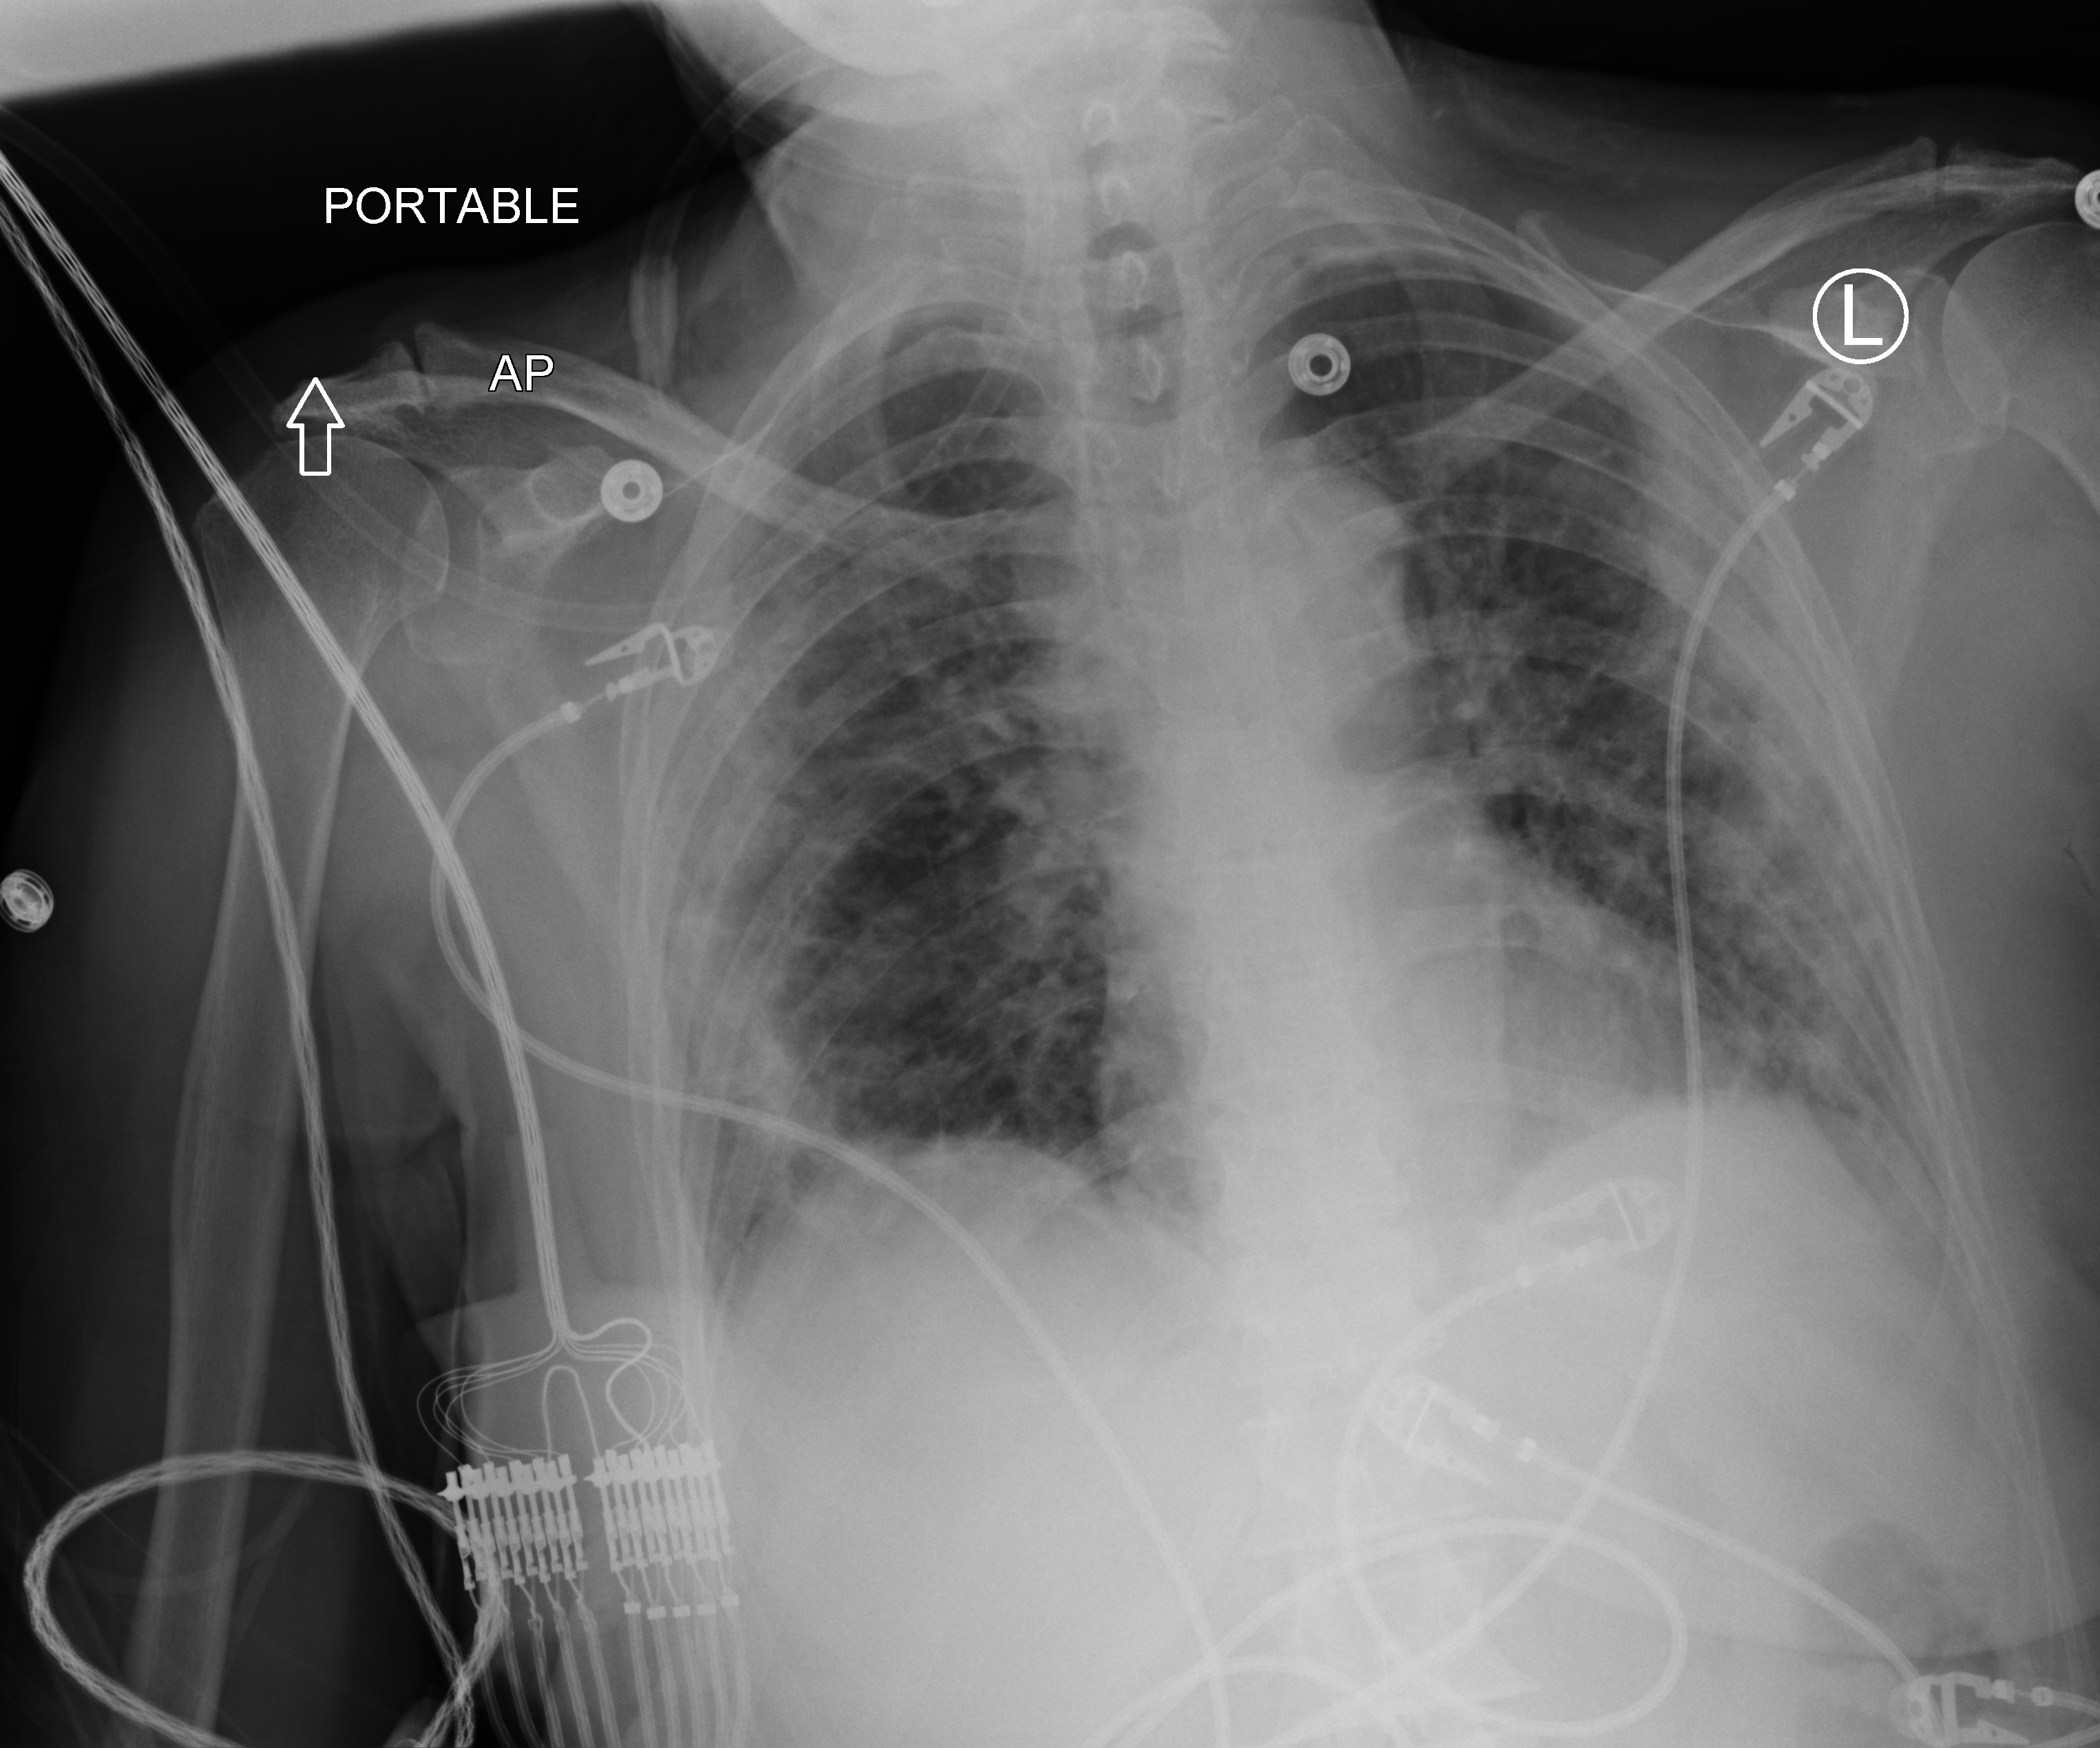
Portable chest radiograph; anteroposterior (AP) projection. Female patient hospitalised with COVID-19, age 60–74 years.
From the hospital-stay record, not from the radiograph (when in the stay this image was taken is not recorded): mechanically ventilated during this hospital stay: yes; diabetes (admission record): no.